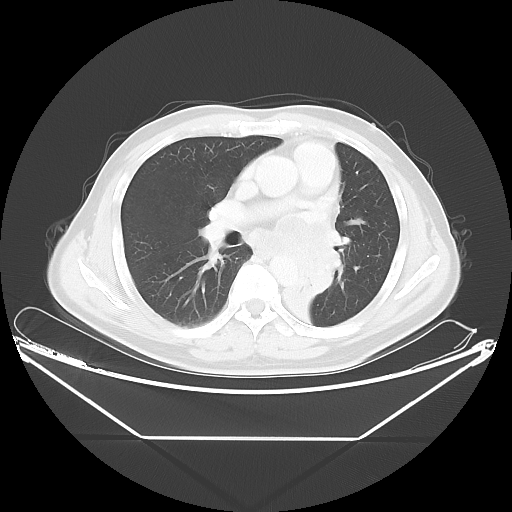
Chest CT, one axial slice. Slice 25 of 48 in the series (ordered by position). Reconstruction kernel LUNG. Lung window (W 1500 / L -600 HU). 5 mm slice thickness. 512 × 512 image matrix. Male patient, age 58 years. From the clinical record (not read from this slice): clinical TNM (as recorded): T3 N3 M0.
Annotated regions visible in this slice (rectangle marked by the reading radiologist):
- lung tumour (recorded histology: squamous cell carcinoma): bounding box <281,235,346,336> (left, top, right, bottom; pixels)